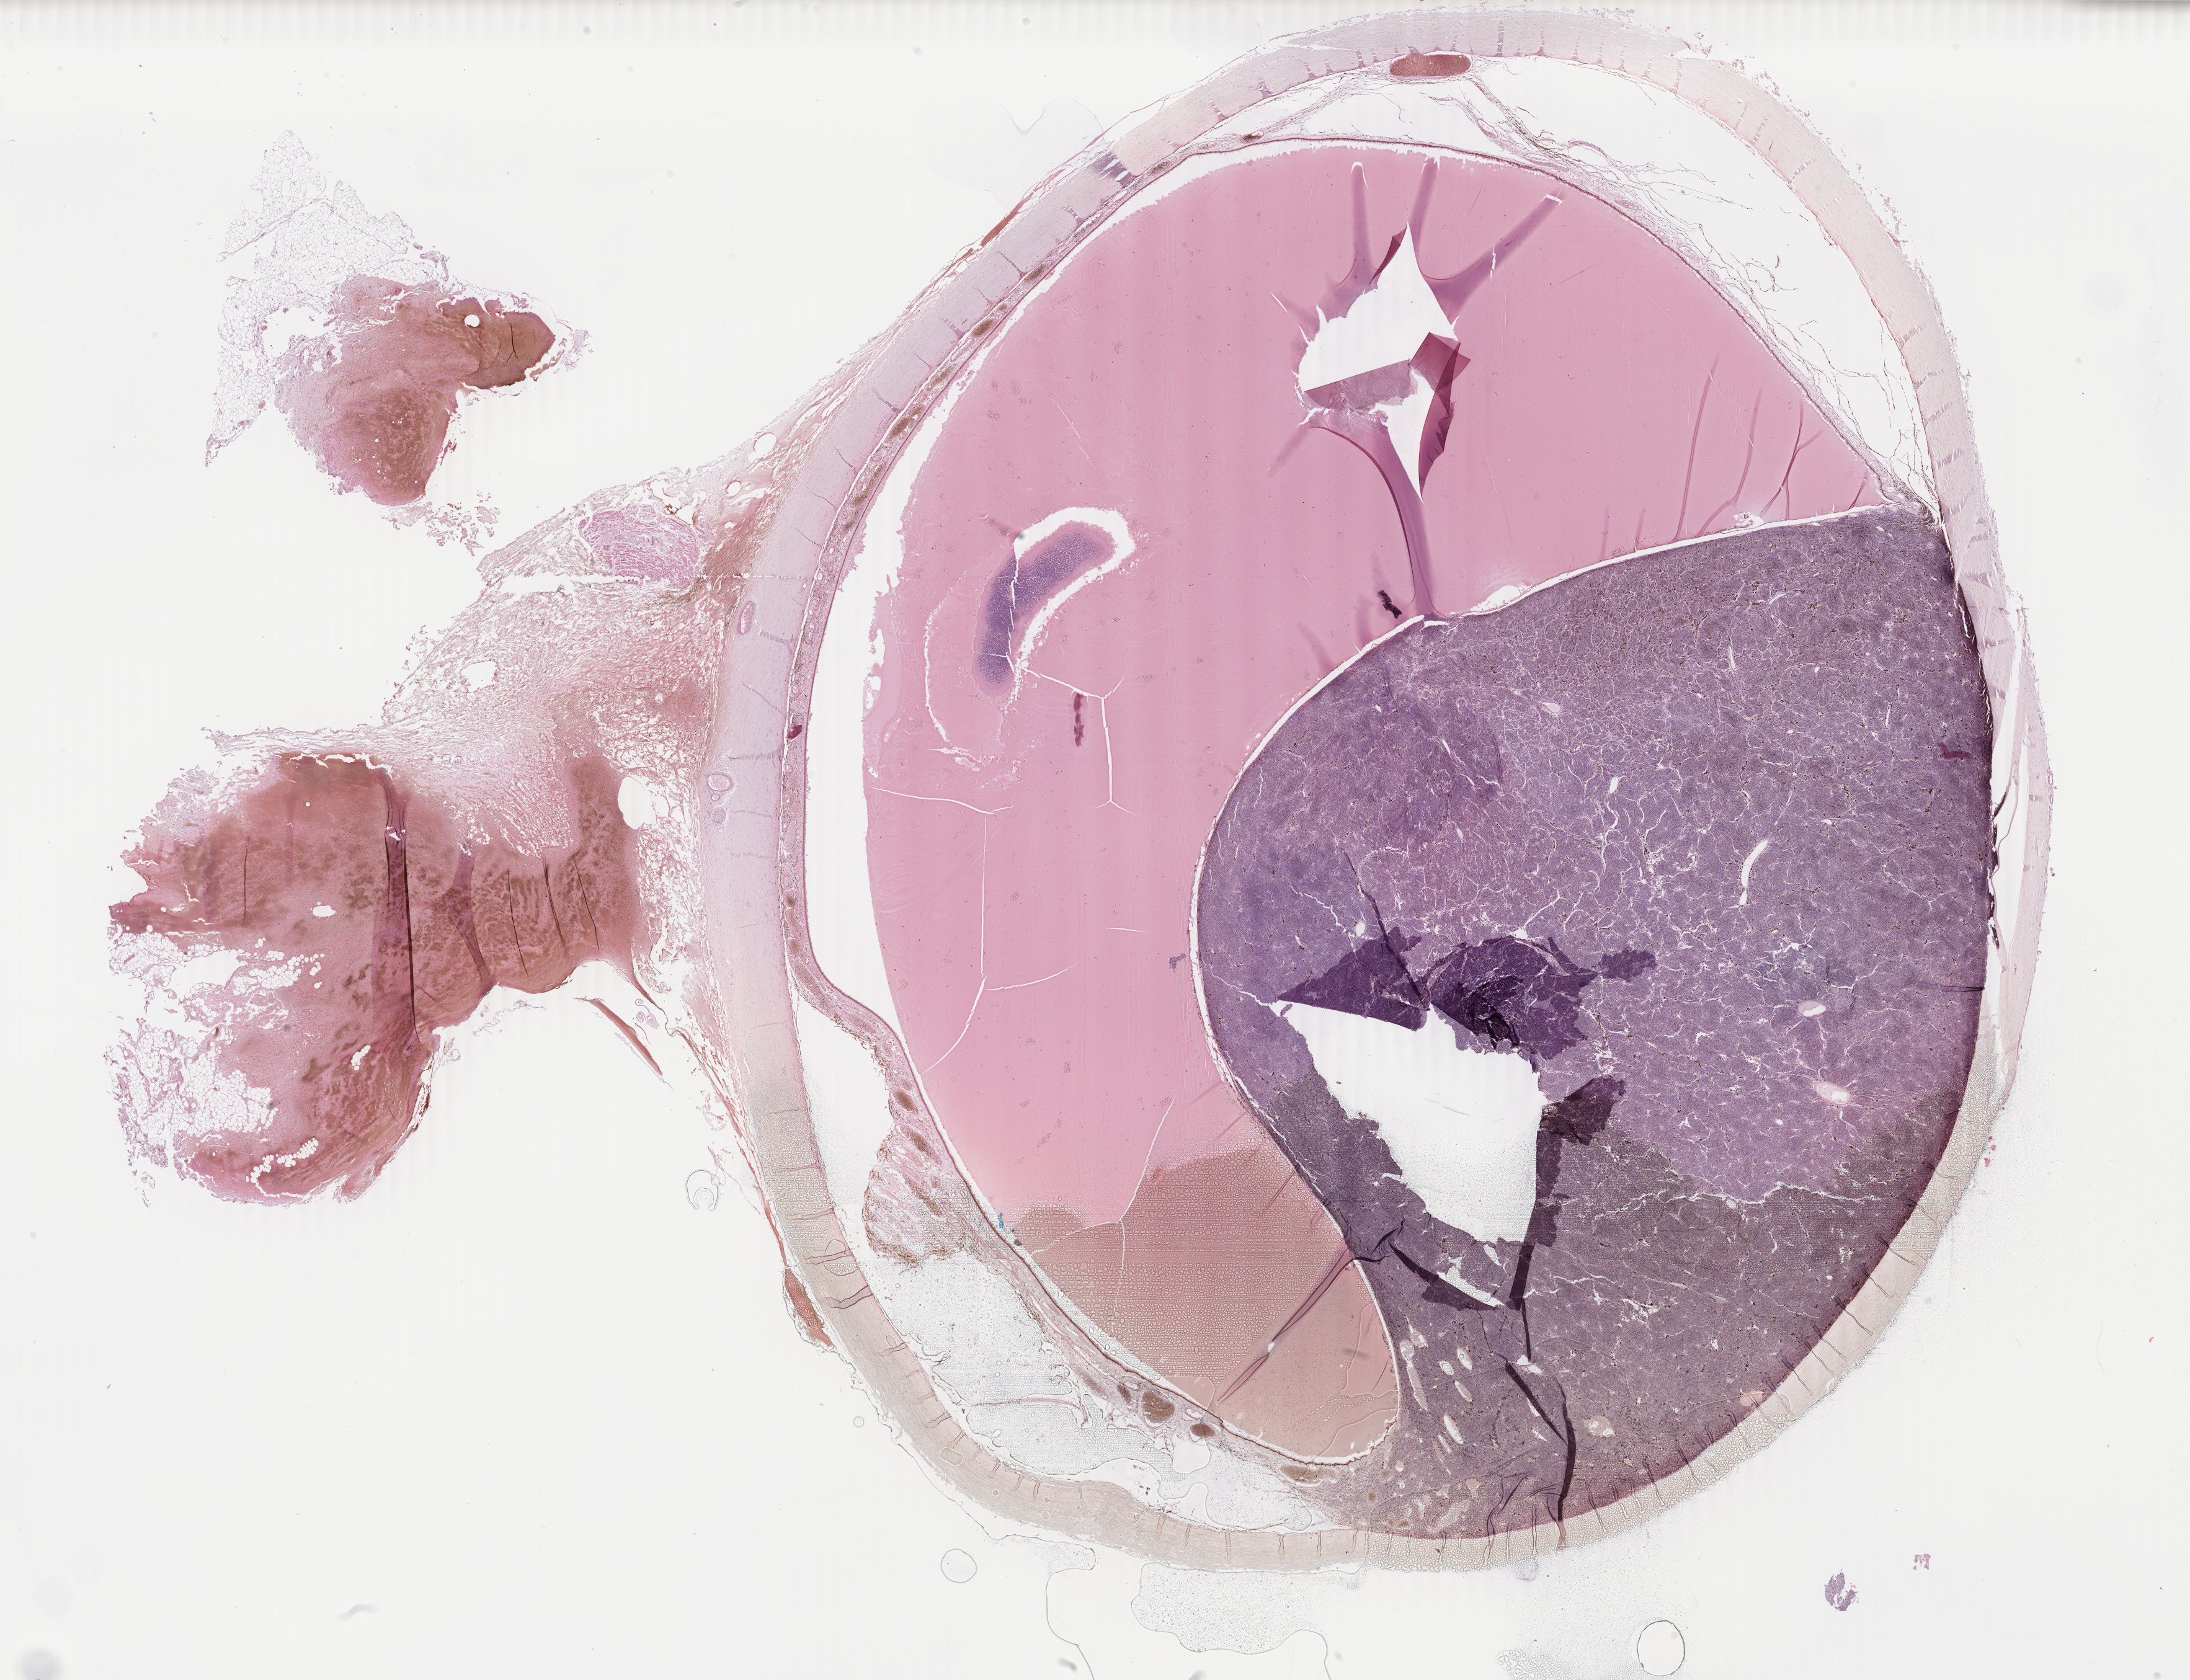
H&E whole-slide image — whole scanned area (about 28.1 x 21.5 mm, slide scanned at 40x) shown as a low-resolution overview. FFPE section. Primary tumour sample from the uvea. Male, age 56 years at initial diagnosis.
AJCC pathologic stage: IIIB. Histologic diagnosis: Spindle cell melanoma, NOS (choroid).